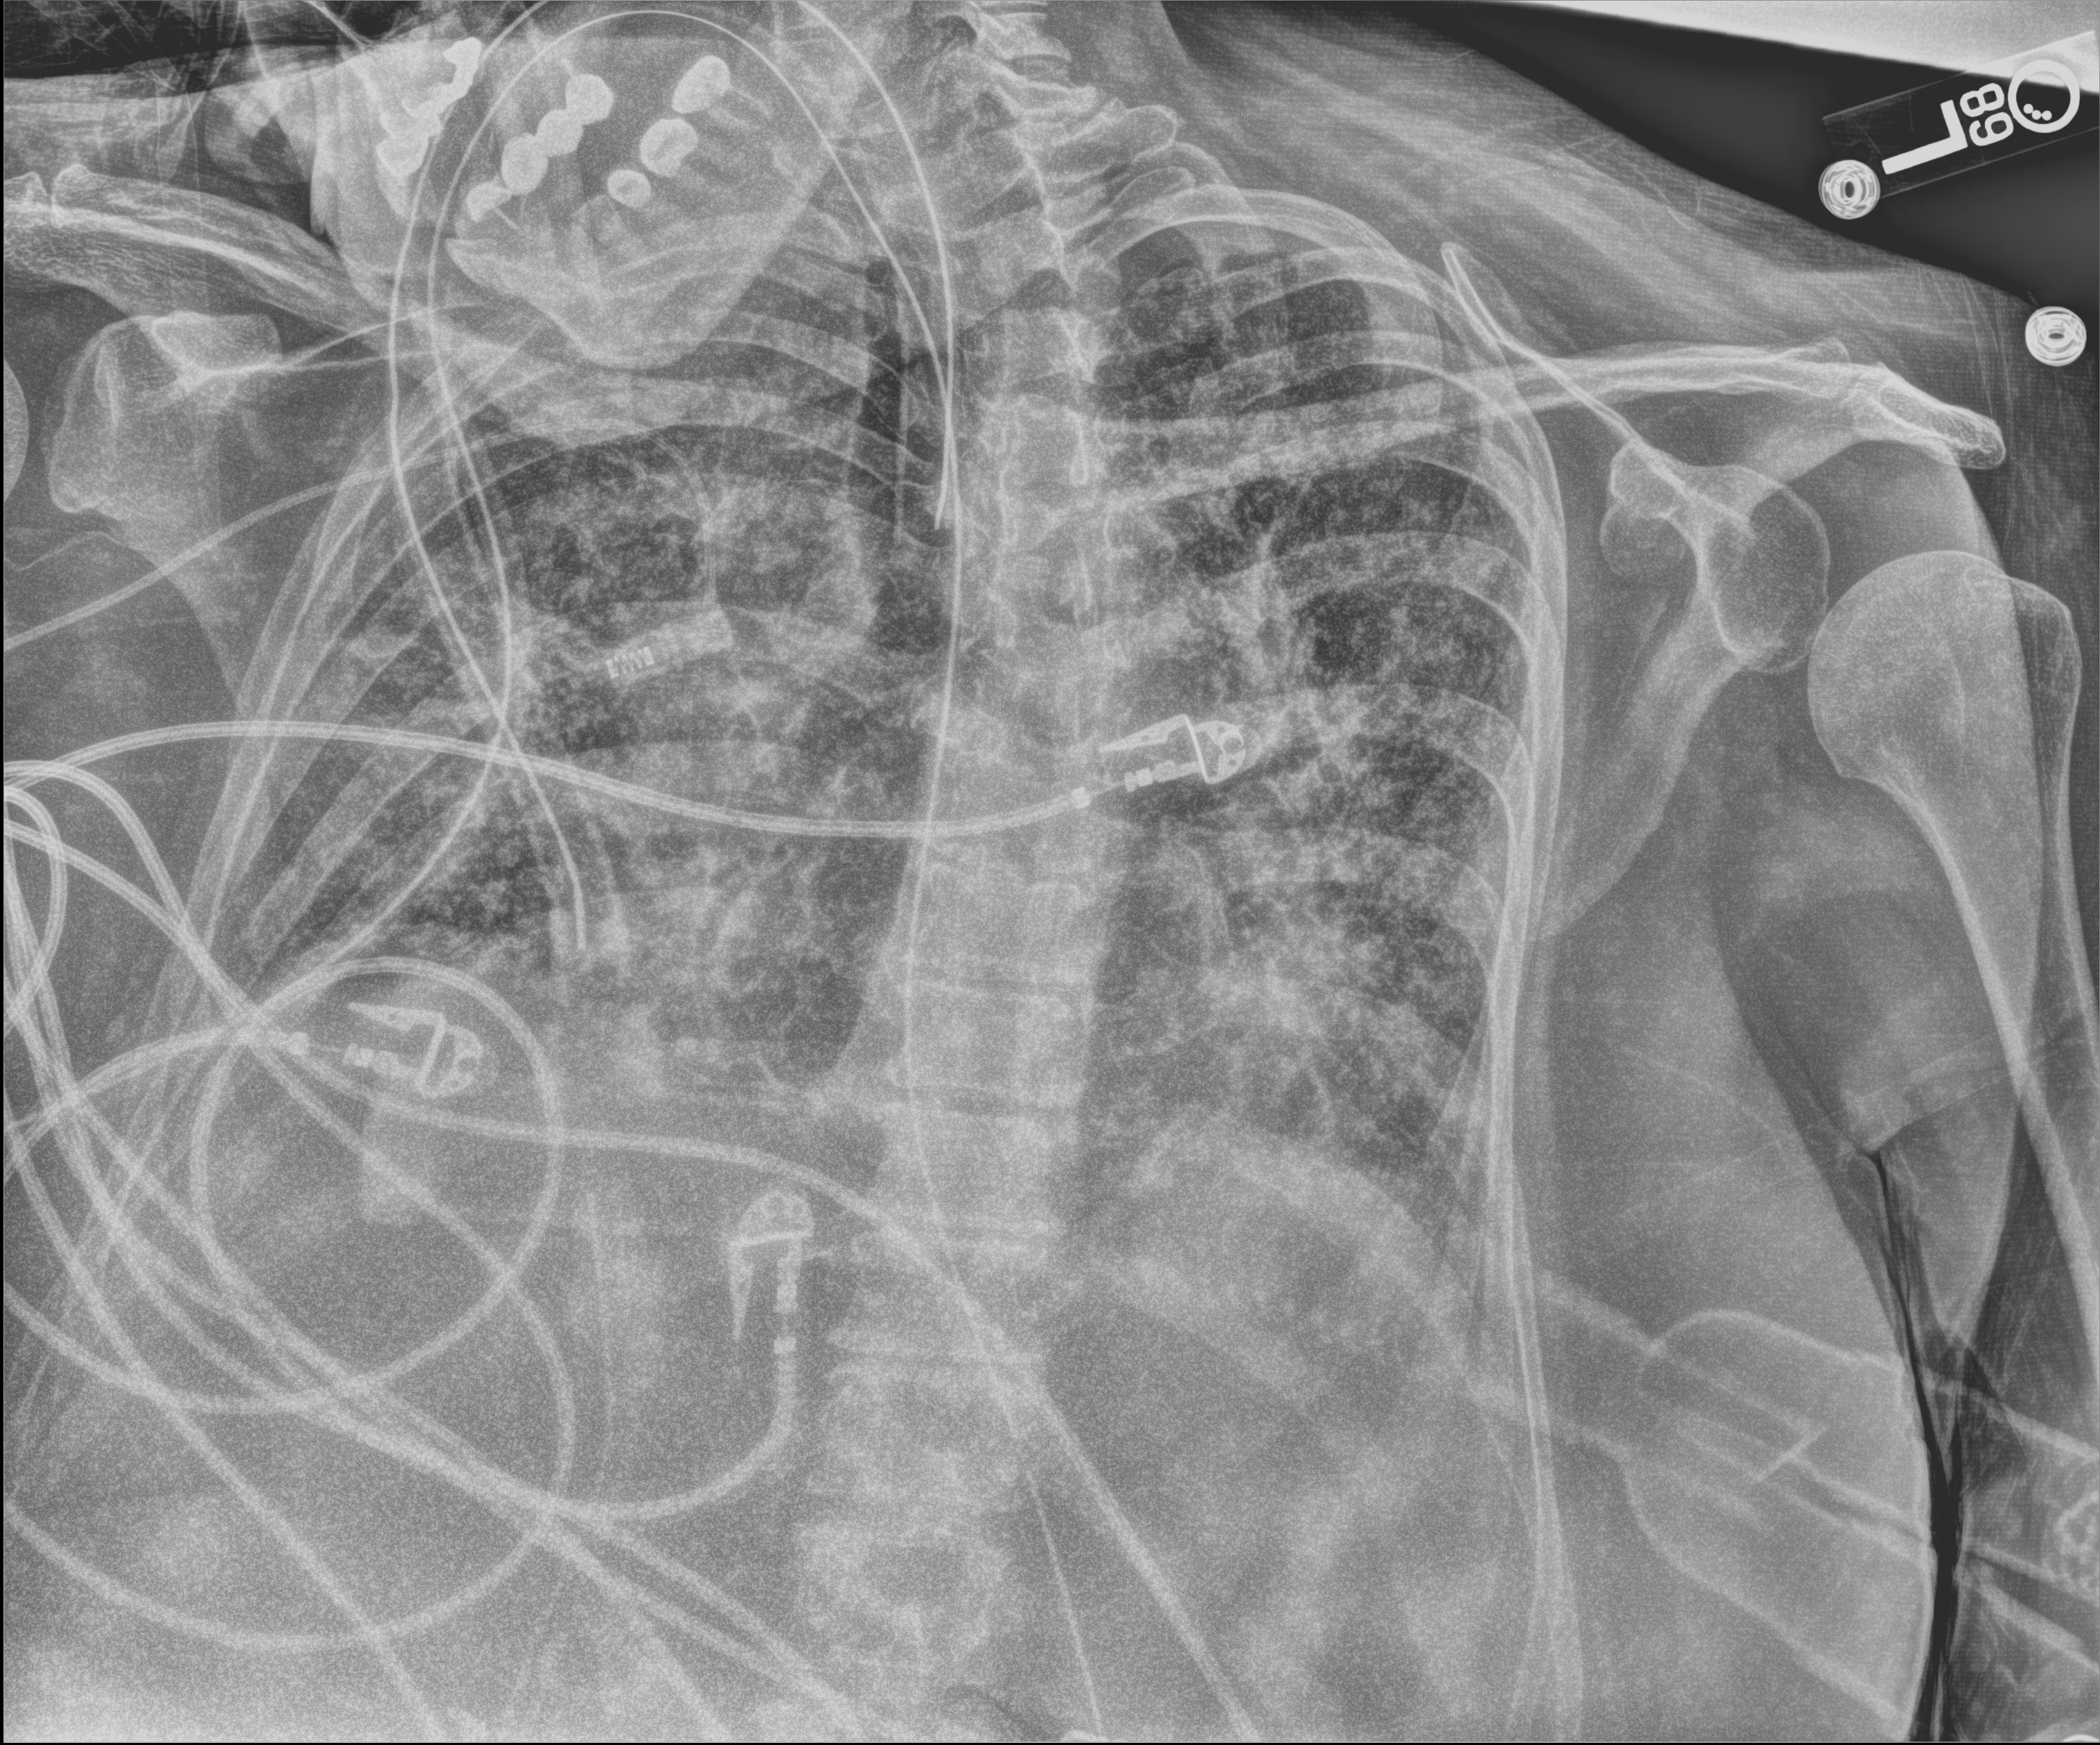
Portable chest radiograph, anteroposterior (AP) projection. Patient hospitalised with COVID-19; female, aged 60–74 years.
Admission-level facts for this patient (not findings on this image; timing relative to this image not recorded): admitted to intensive care during this hospital stay: yes.